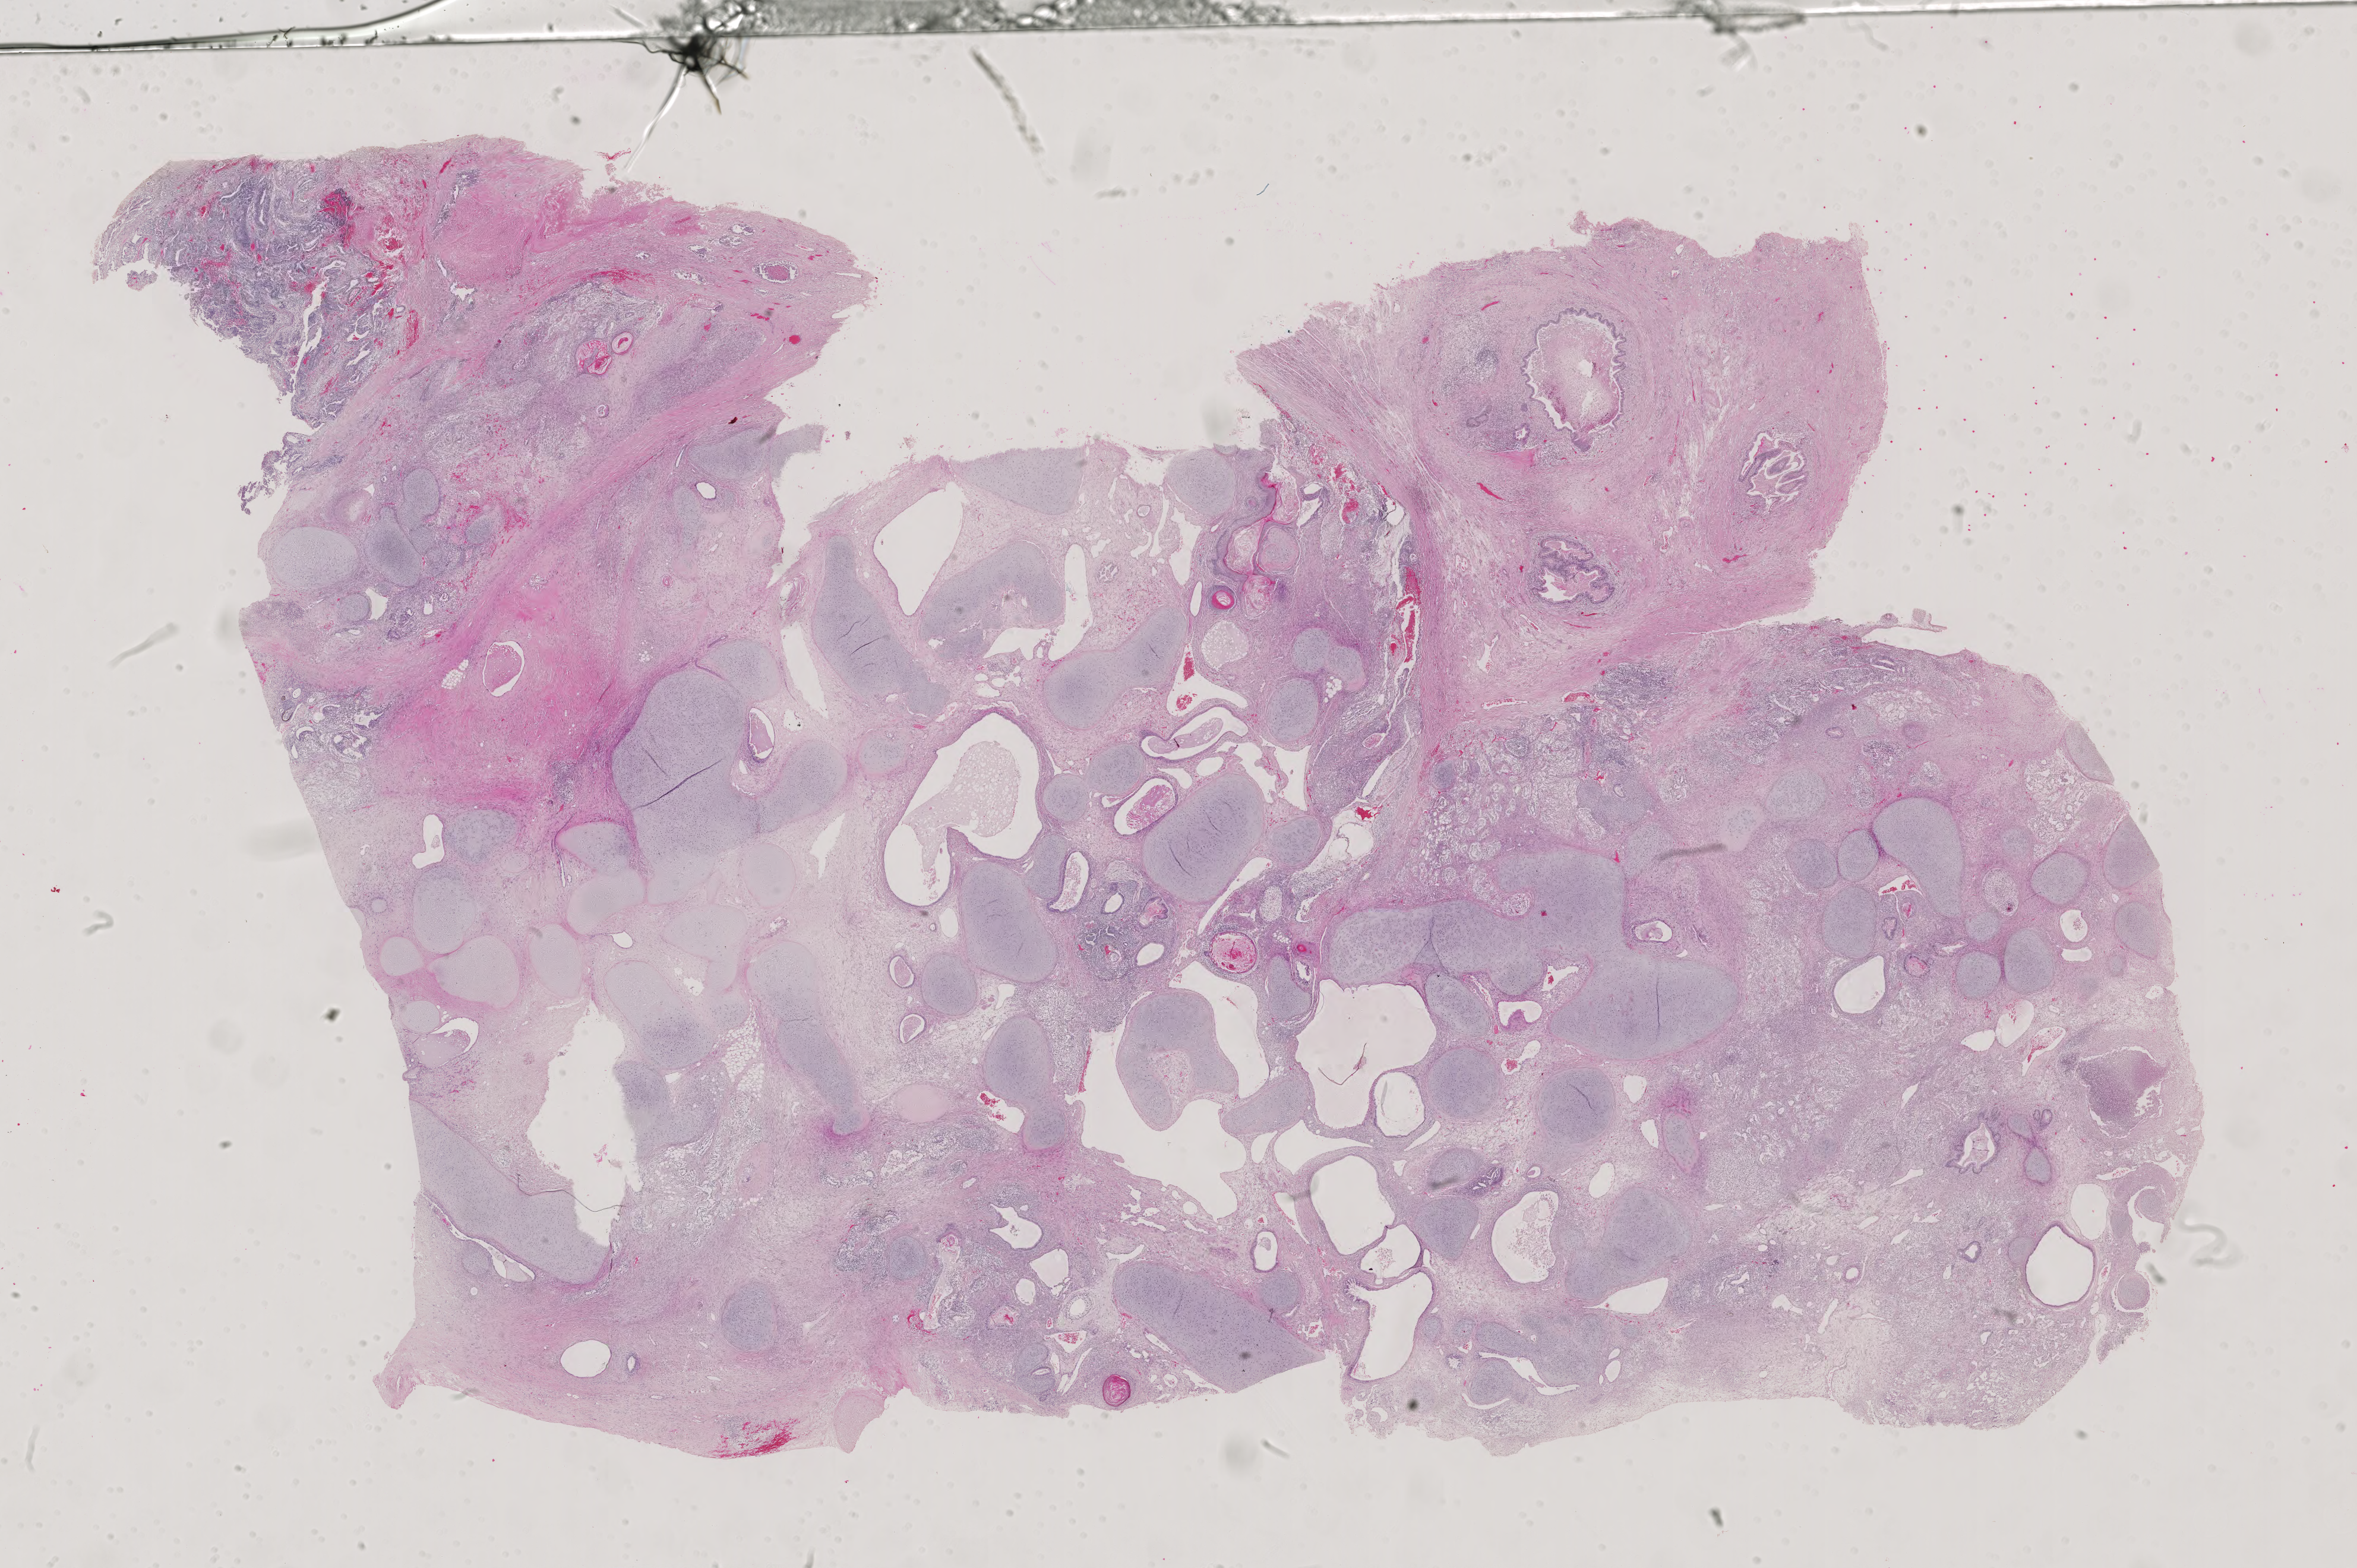
Whole-slide histology image, H&E-stained — whole scanned area (about 28.9 x 19.2 mm, from a 40x scan) shown as a low-resolution overview, formalin-fixed paraffin-embedded (FFPE) diagnostic section, sample: primary tumour, testis. Male patient; age at initial diagnosis 20 years.
- pathologic diagnosis: Mixed germ cell tumor
- laterality: left
- AJCC pathologic stage: IIIC (6th edition)